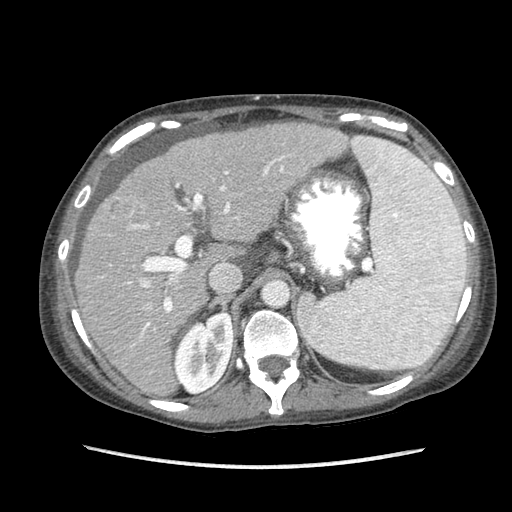
Contrast-enhanced abdominal CT (liver protocol), one axial slice. Reconstruction kernel STANDARD. Soft-tissue window (W 400 / L 40 HU). 2.5 mm slice thickness. 512 × 512 image matrix. Case-level facts recorded for this patient, not image findings: diagnosis: hepatocellular carcinoma (patient treated with transarterial chemoembolisation; whether this scan precedes or follows treatment is not stated here); TNM stage (as recorded): Stage-IIIB; Child-Pugh class: A; tumour nodularity: uninodular.
Annotated regions visible in this slice (semi-automatically segmented with operator editing):
- abdominal aorta: bounding box <263,280,289,306> (left, top, right, bottom; pixels)
- liver parenchyma outside the tumour (the mass and vessels are separate outlines, so this box may not span the whole liver): <74,122,367,396>
- mass: <104,198,135,222>
- liver vessels: <129,138,366,345>